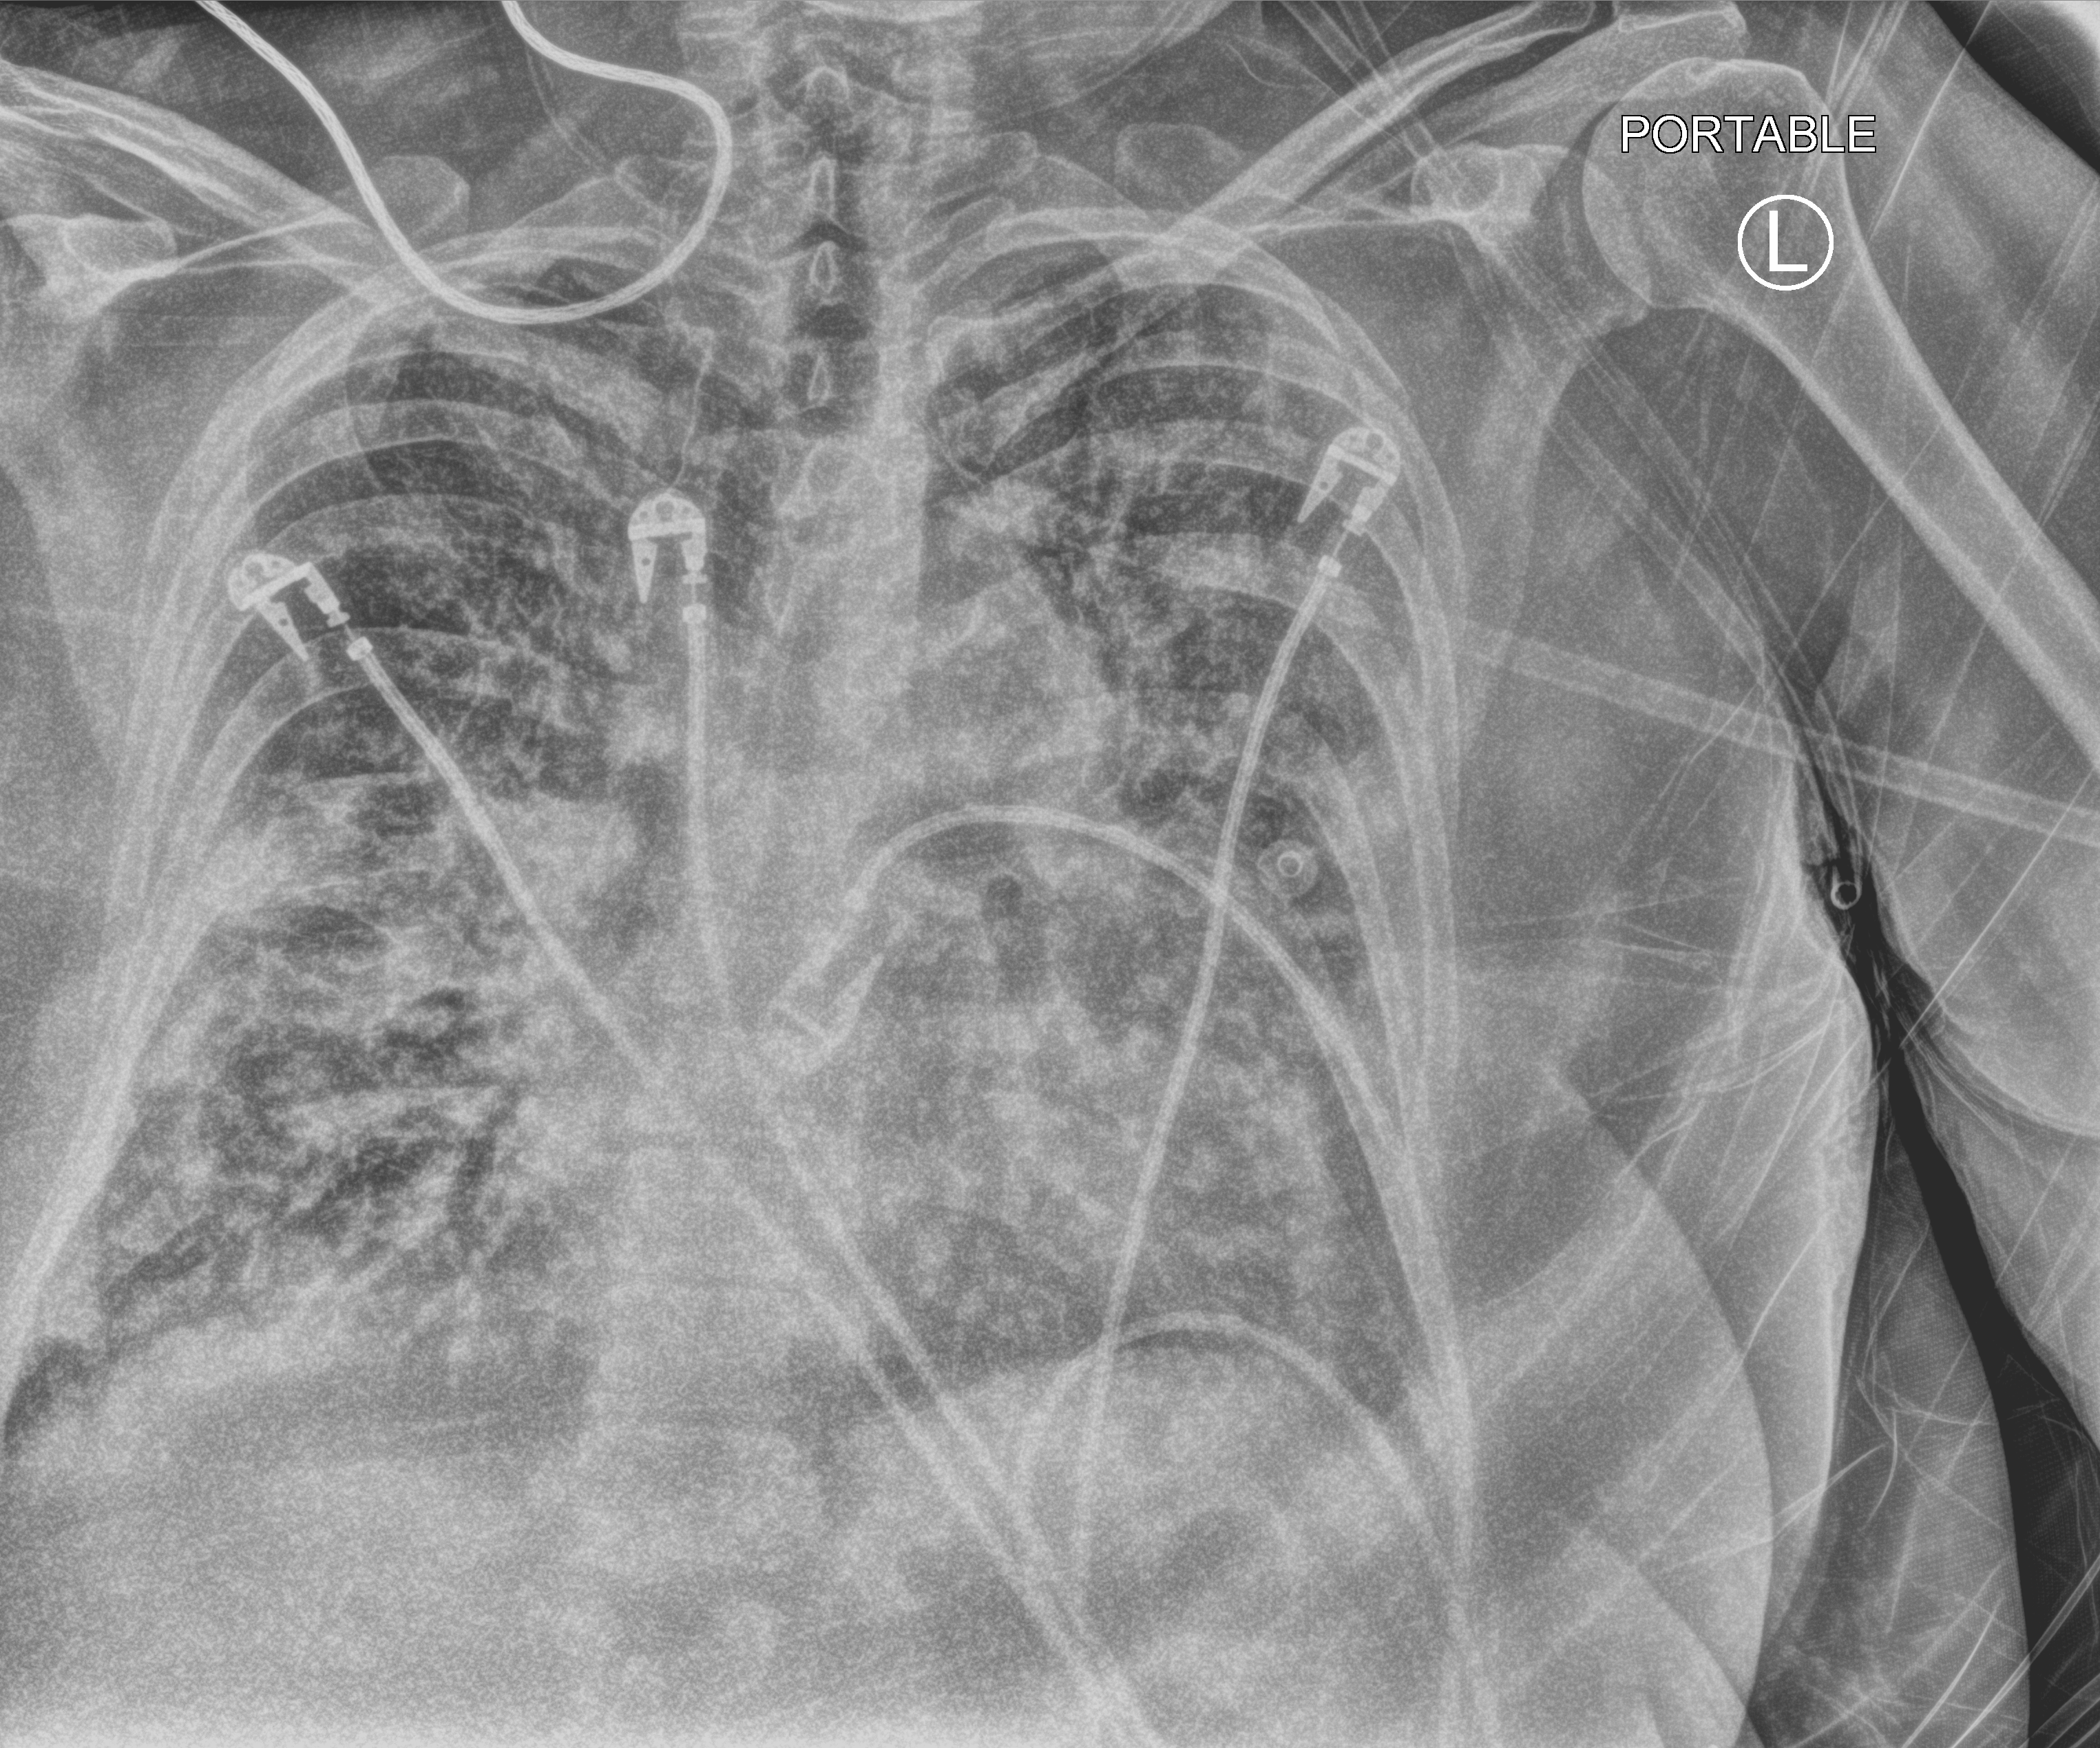
Bedside chest radiograph (computed radiography); anteroposterior (AP) projection. Female patient hospitalised with COVID-19, age 60–74 years.
From the hospital-stay record, not from the radiograph (when in the stay this image was taken is not recorded):
- chronic kidney disease (admission record): no